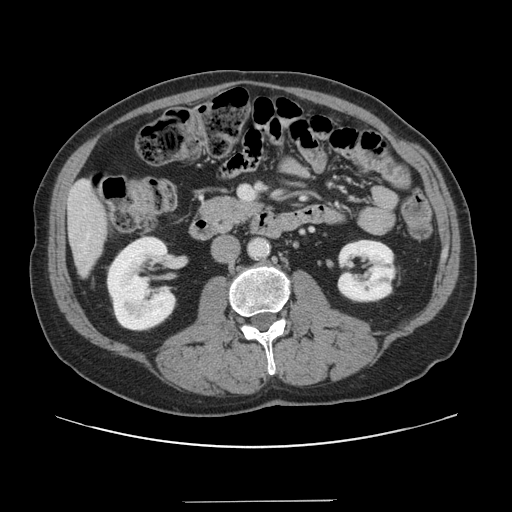
Contrast-enhanced abdominal CT, one axial slice. Slice 45 of 151 in the series (ordered by position). Intravenous contrast given. Soft-tissue window (W 400 / L 40 HU). 2.5 mm slice thickness. 512 × 512 image matrix, field of view 399 × 399 mm. Male patient, age 63 years. Case-level facts recorded for this patient, not image findings: diagnosis: colorectal cancer liver metastases, imaged before liver resection; multiple liver metastases: no; largest metastasis: 2.1 cm; disease in both lobes: no.
Structures marked on this image (expert manual segmentation):
- liver: box from (x=69, y=182) to (x=107, y=273) px
- planned liver remnant (the part of the liver to remain after resection): (x=69, y=182)–(x=108, y=273)
- portal vein (with intrahepatic branches): (x=240, y=186)–(x=253, y=199)